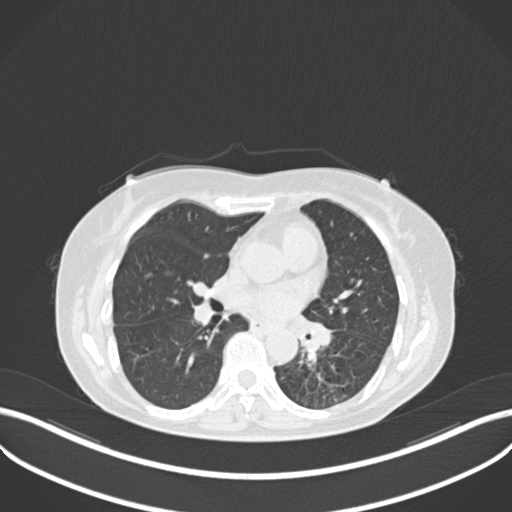
Chest CT, one axial slice. Position 133 of 270 along the scan axis. 120 kVp. Lung window (W 1500 / L -600 HU). 1 mm slice thickness. 512 × 512 image matrix, field of view 400 × 400 mm. Patient: female, 63 years. From the clinical record (not read from this slice): clinical TNM (as recorded): T1b N0 M0.
Outlined on this slice (rectangle marked by the reading radiologist):
- lung tumour (recorded histology: adenocarcinoma): bounding box [x1, y1, x2, y2] px = [292, 321, 340, 364]